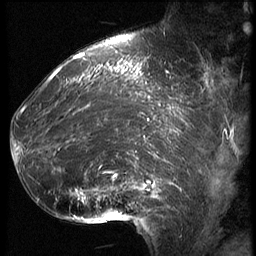
Breast MRI (dynamic contrast-enhanced), one sagittal slice. Position 21 of 62 along the scan axis. 3 images stored at this slice position (order not interpretable as contrast timing). 1.5 T. TE 4.2 ms, TR 9 ms. 2.5 mm slice thickness. 256 × 256 image matrix, field of view 180 × 180 mm. Female patient, age 39 years. From the clinical record (not read from this slice): setting: breast cancer imaged before/during neoadjuvant chemotherapy; receptor status: HER2-positive.
Structures marked on this image (semi-automatic segmentation, software-assisted and operator-edited):
- analysis volume of interest (the breast-tissue region the enhancement analysis was run in; not a lesion): bounding box (x1, y1, x2, y2) in pixels: (16, 64, 171, 228)
- tumour enhancement mask (voxels above the 140 % enhancement threshold inside the analysis volume of interest): (16, 64, 171, 203)